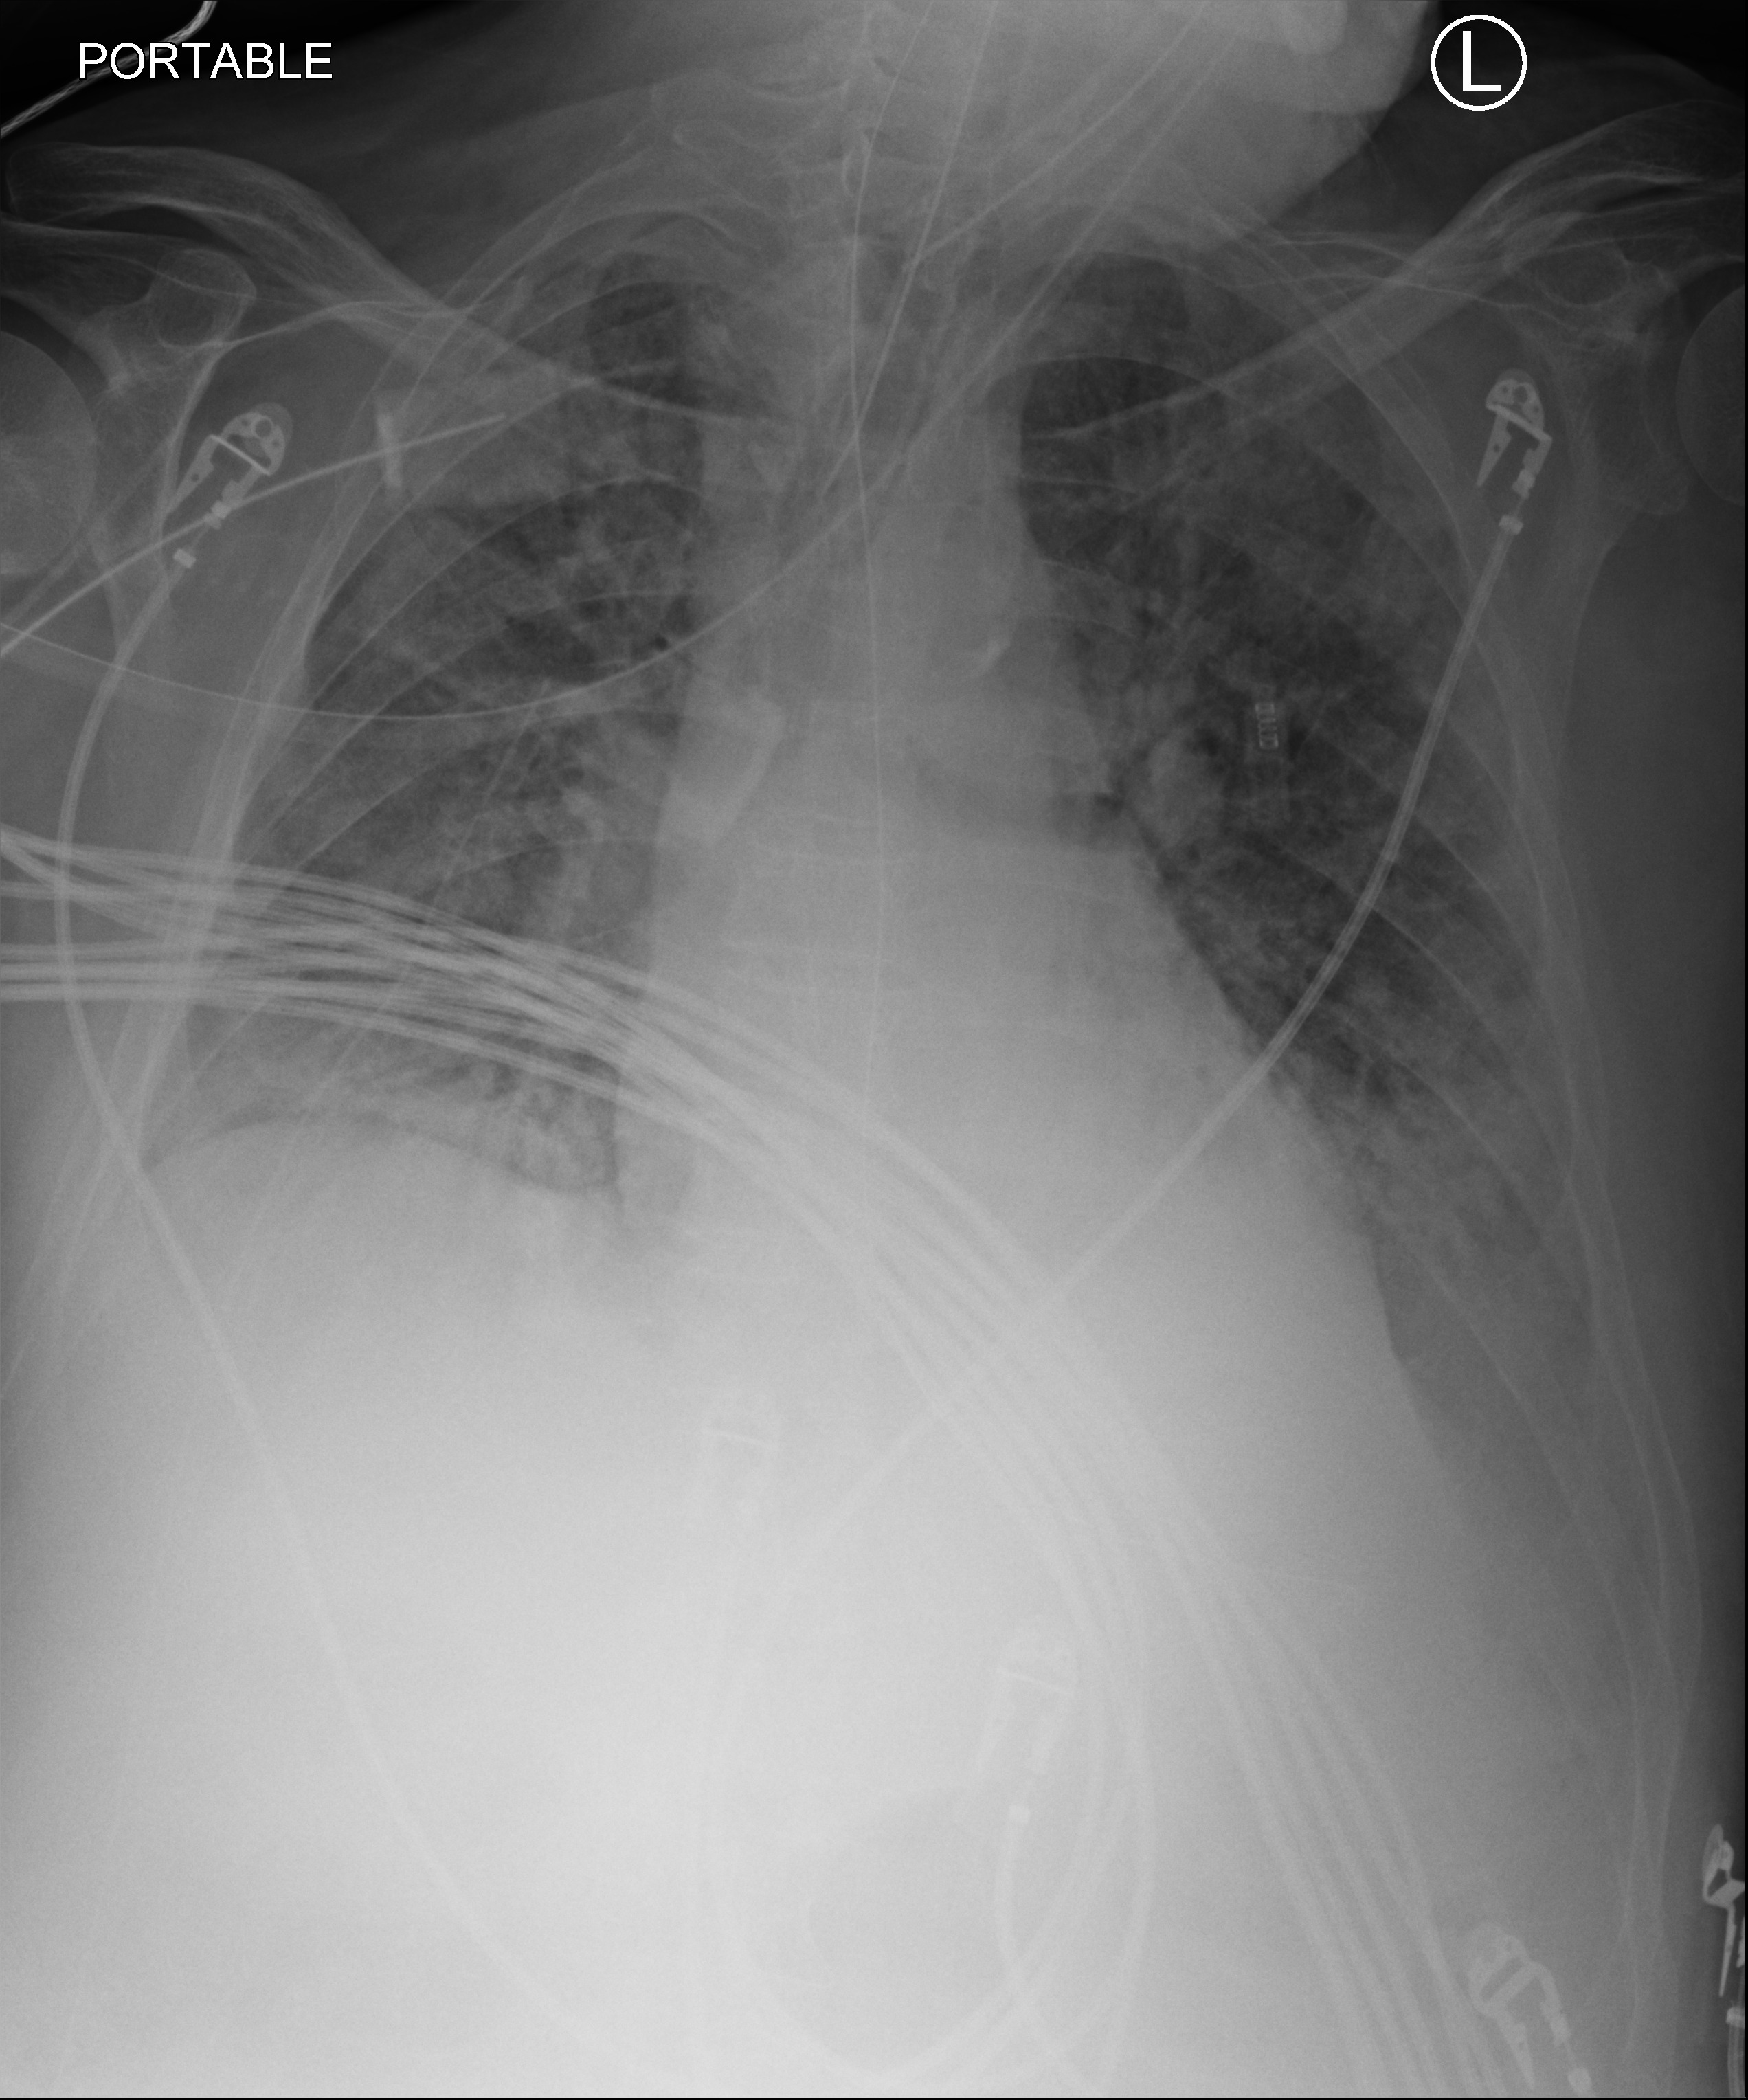
Chest X-ray (portable). Patient hospitalised with COVID-19; male, aged 60–74 years.
Admission-level facts for this patient (not findings on this image; timing relative to this image not recorded):
- mechanically ventilated during this hospital stay: yes